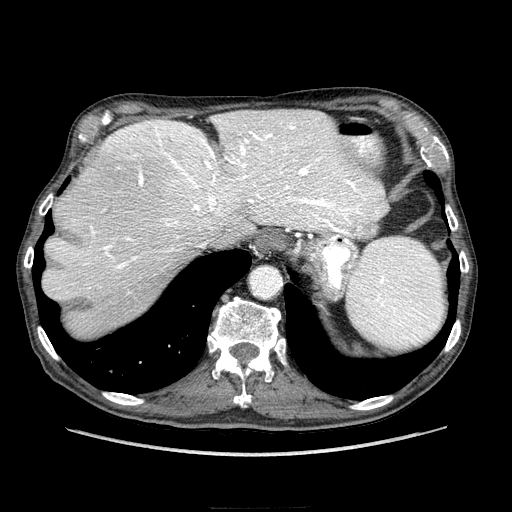
Contrast-enhanced abdominal CT (liver protocol), one axial slice. Position 177 of 218 along the scan axis. Reconstruction kernel STANDARD. 100 kVp. Soft-tissue window (W 400 / L 40 HU). 2.5 mm slice thickness. 512 × 512 image matrix, field of view 380 × 380 mm. From the clinical record (not read from this slice): diagnosis: hepatocellular carcinoma (patient treated with transarterial chemoembolisation; whether this scan precedes or follows treatment is not stated here); TNM stage (as recorded): Stage-IIIA; Child-Pugh class: A.
Structures marked on this image (semi-automatically segmented with operator editing):
- abdominal aorta: bounding box [x1, y1, x2, y2] px = [249, 267, 280, 296]
- liver parenchyma outside the tumour (the mass and vessels are separate outlines, so this box may not span the whole liver): [44, 110, 386, 336]
- liver vessels: [50, 118, 382, 294]